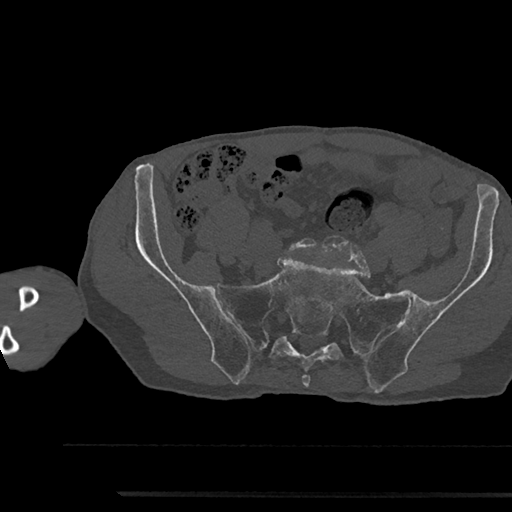
CT including the spine, one axial slice. Slice 278 of 797 in the series (ordered by position). 120 kVp. Bone window (W 1800 / L 400 HU). 0.5 mm slice thickness. 512 × 512 image matrix, field of view 367 × 367 mm. Patient: male, 79 years. Case-level facts recorded for this patient, not image findings: primary cancer: prostate.
Outlined on this slice (semi-automatic segmentation, software-assisted and operator-edited):
- L5 vertebra: bounding box (x1, y1, x2, y2) in pixels: (289, 238, 317, 251)